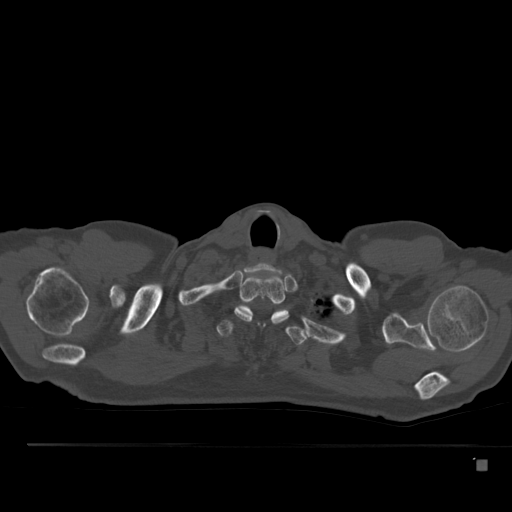
CT including the spine, one axial slice; position 422 of 517 along the scan axis; bone window (W 1800 / L 400 HU); 1.5 mm slice thickness; 512 × 512 image matrix, field of view 408 × 408 mm. Patient: male, 70 years. Case-level facts recorded for this patient, not image findings: primary cancer: renal; vertebrae with lytic lesions (as recorded): T4, T6, T10, T12, L3, L4, L5.
Annotated regions visible in this slice (semi-automatically segmented with operator editing):
- T1 vertebra: box from (x=235, y=274) to (x=289, y=324) px
- T2 vertebra: (x=217, y=304)–(x=308, y=345)